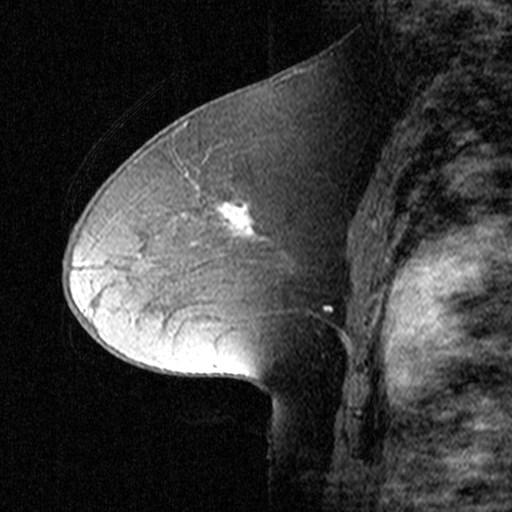
Breast MRI (dynamic contrast-enhanced), one sagittal slice; slice 23 of 44 in the series (ordered by position); dynamic contrast-enhanced study with each time point stored as its own series, time point 2 of 3 at this slice position (early post-contrast, ordered by acquisition time); 1.5 T; TE 4.5 ms, TR 11 ms; 3 mm slice thickness; 512 × 512 image matrix. Patient: female, 50 years. From the clinical record (not read from this slice): setting: breast cancer imaged before/during neoadjuvant chemotherapy; receptor status: HR-positive, HER2-negative.
Outlined on this slice (semi-automatic segmentation, software-assisted and operator-edited):
- analysis volume of interest (the breast-tissue region the enhancement analysis was run in; not a lesion): bounding box (x1, y1, x2, y2) in pixels: (154, 164, 313, 287)
- tumour enhancement mask (voxels above the 90 % enhancement threshold inside the analysis volume of interest): (222, 203, 252, 234)